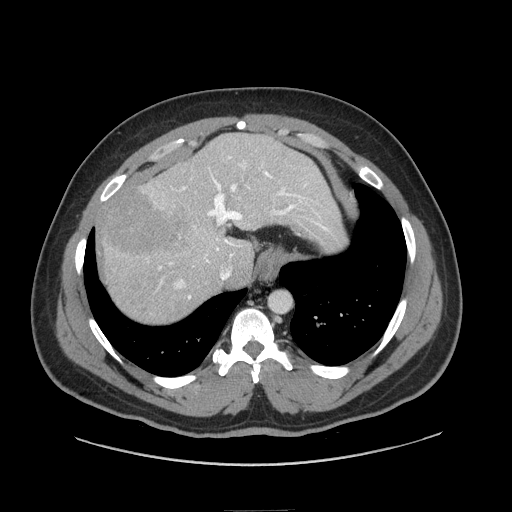
Contrast-enhanced abdominal CT (liver protocol), one axial slice. Slice 62 of 87 in the series (ordered by position). 140 kVp. Soft-tissue window (W 400 / L 40 HU). 2.5 mm slice thickness. 512 × 512 image matrix. From the clinical record (not read from this slice): diagnosis: hepatocellular carcinoma (patient treated with transarterial chemoembolisation; whether this scan precedes or follows treatment is not stated here); TNM stage (as recorded): Stage-II; Child-Pugh class: A.
Structures marked on this image (semi-automatically segmented with operator editing):
- liver parenchyma outside the tumour (the mass and vessels are separate outlines, so this box may not span the whole liver): box from (x=98, y=134) to (x=346, y=322) px
- mass: (x=99, y=184)–(x=191, y=260)
- liver vessels: (x=112, y=156)–(x=328, y=299)